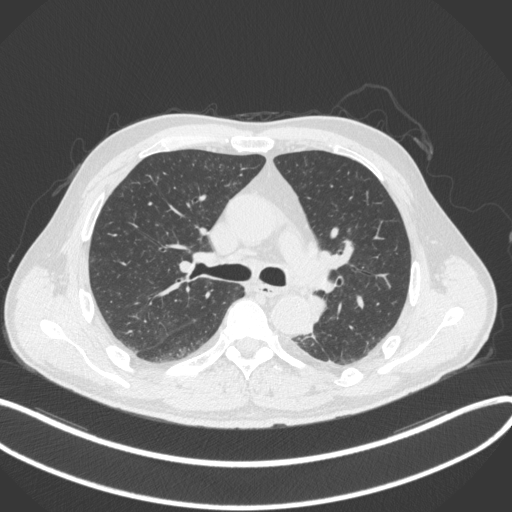
Chest CT, one axial slice. Position 222 of 328 along the scan axis. Lung window (W 1500 / L -600 HU). 512 × 512 image matrix. Patient: male, 59 years. From the clinical record (not read from this slice): clinical TNM (as recorded): T2a N2 M0.
Annotated regions visible in this slice (bounding box drawn by a radiologist):
- lung tumour (recorded histology: squamous cell carcinoma): bounding box [x1, y1, x2, y2] px = [306, 293, 329, 327]